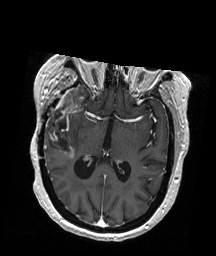
Brain MRI from a brain-tumour surgery series, one axial slice. Slice 105 of 192 in the series (ordered by position). T1-weighted post-contrast. 1 mm slice thickness. 216 × 256 image matrix. From the clinical record (not read from this slice): histopathology: Glioblastoma; WHO grade: 4; IDH mutation: no.
Outlined on this slice (expert manual segmentation):
- tumour: bounding box [x1, y1, x2, y2] px = [50, 87, 87, 139]